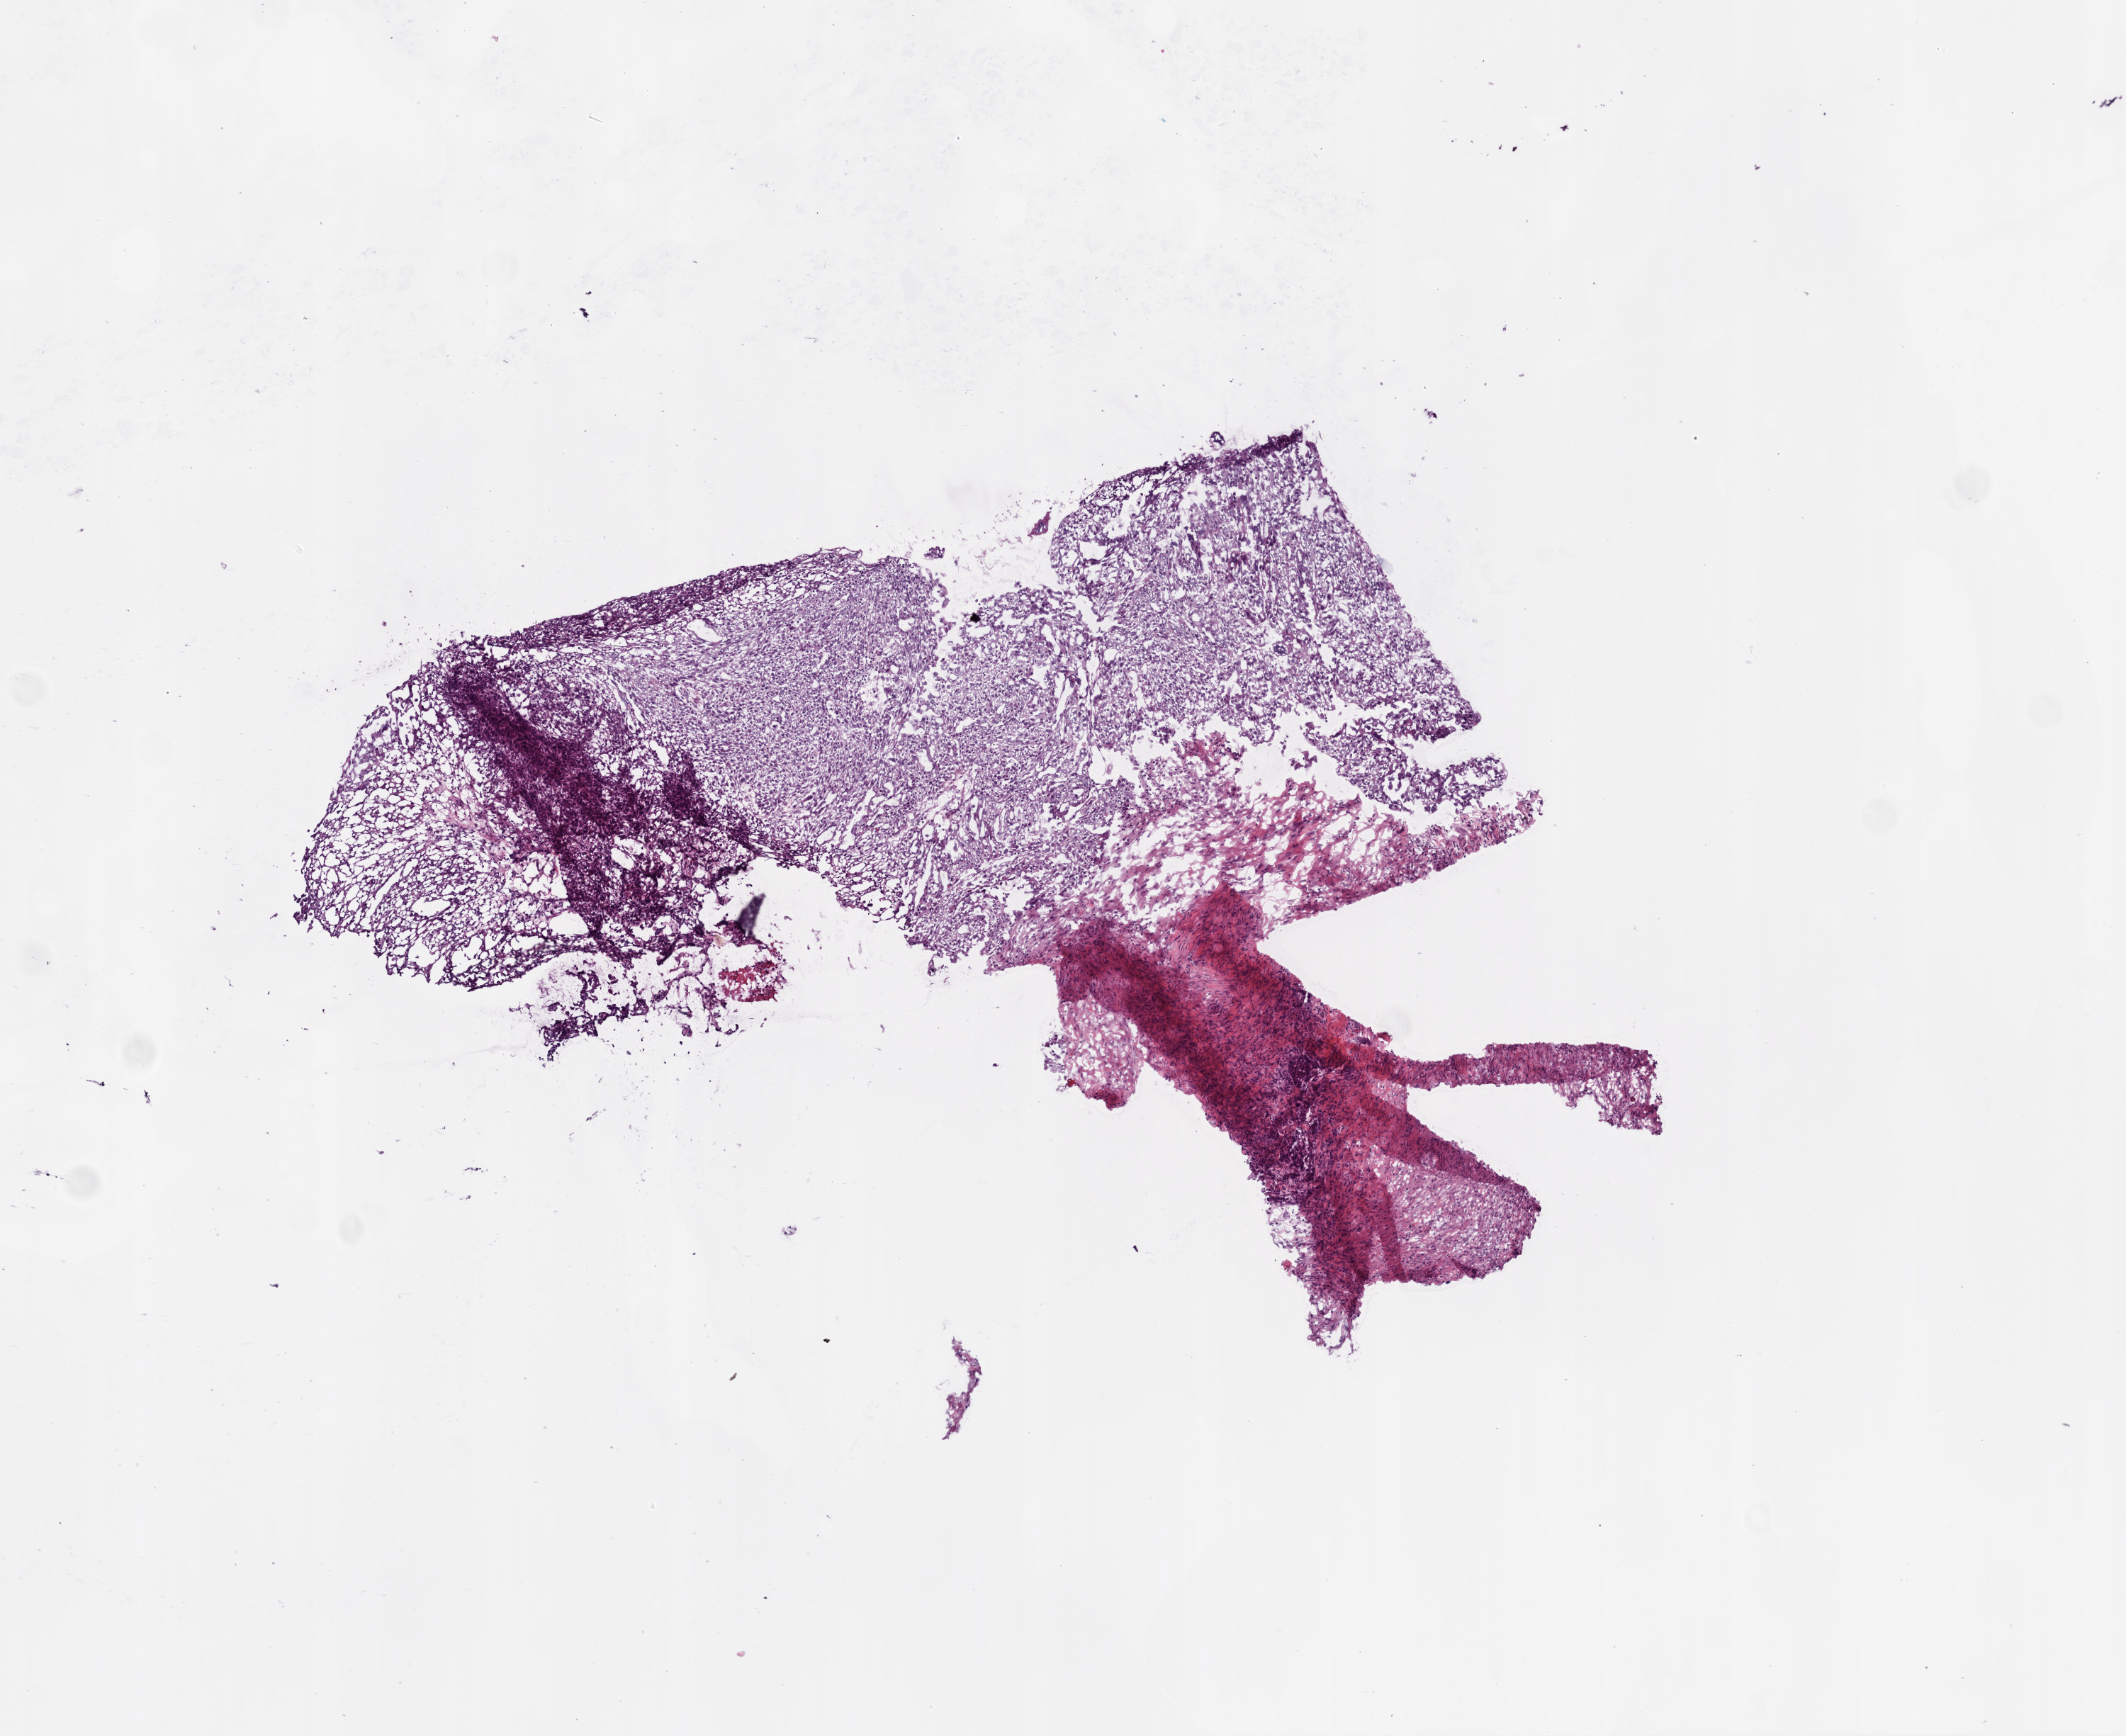
H&E-stained whole-slide image — a low-resolution overview of the entire scanned area, about 6.0 x 4.9 mm (from a 20x scan); frozen section from the bottom of the tissue portion; ovary, primary tumour sample. Female patient; age at initial diagnosis 45 years.
Histologic diagnosis: Serous cystadenocarcinoma, NOS.